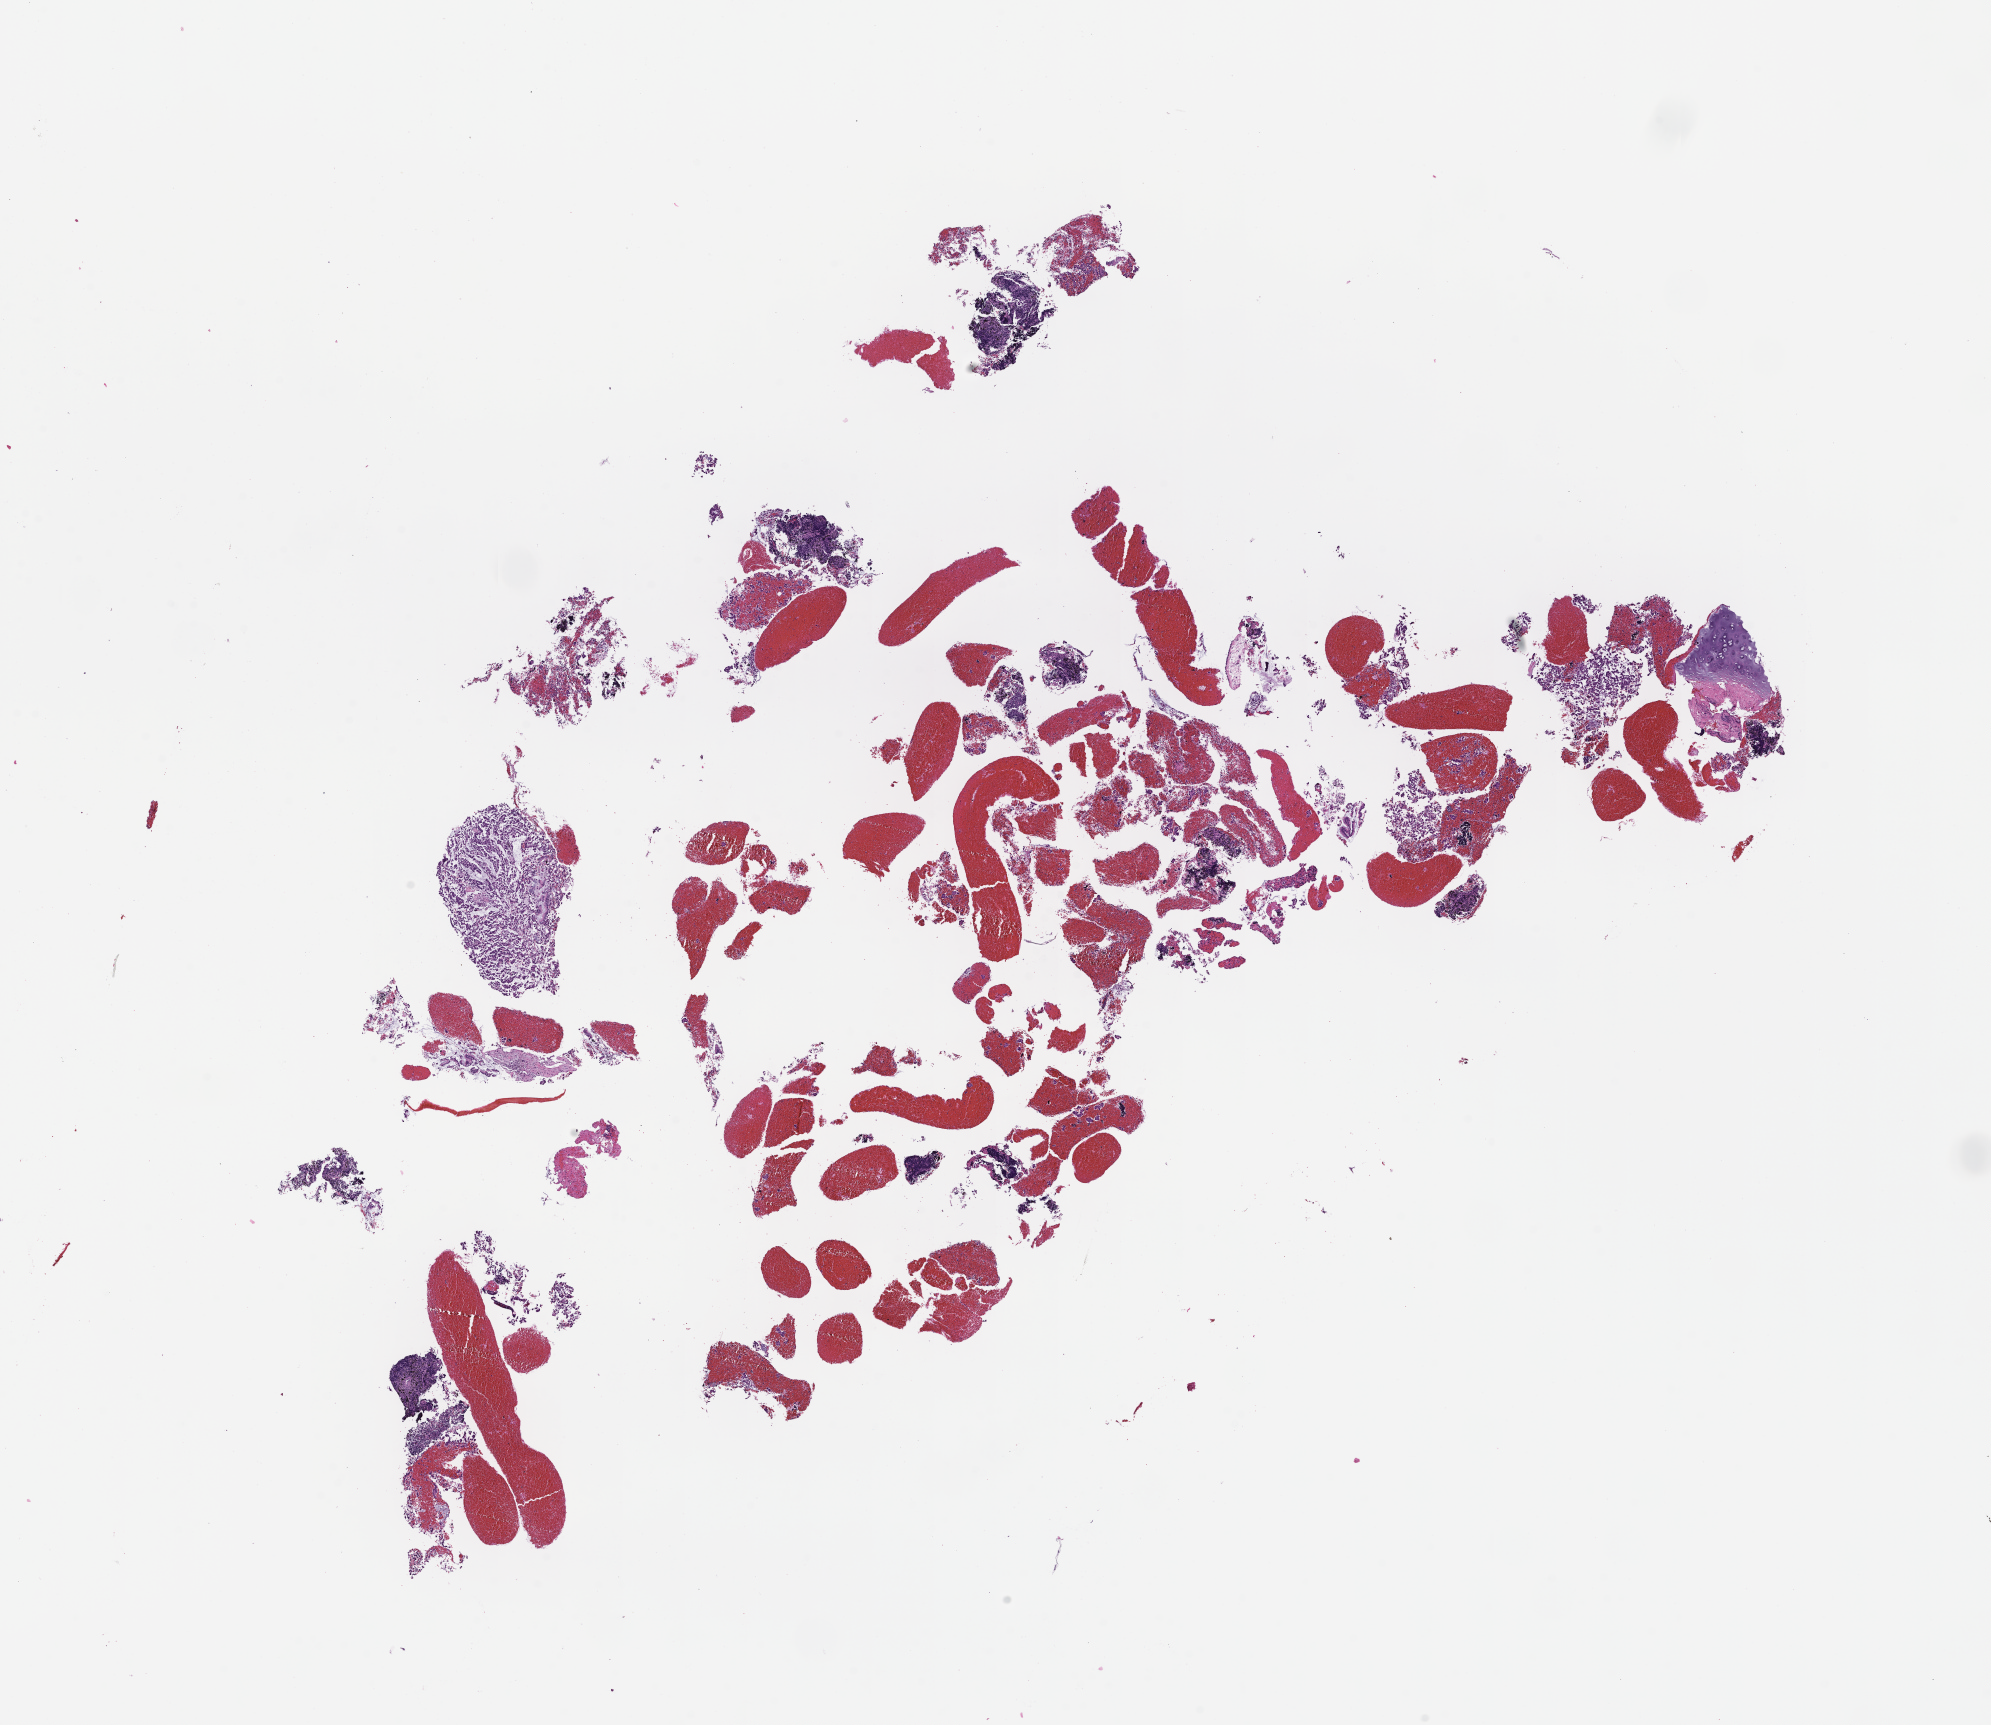
Haematoxylin and eosin whole-slide image — shown as a low-resolution overview of the whole scanned area (about 16.1 x 13.9 mm), FFPE section. Patient sex: female.
This section: metastasis (sampled organ not recorded). Primary diagnosis of the patient: Non-Small Cell Lung Carcinoma.